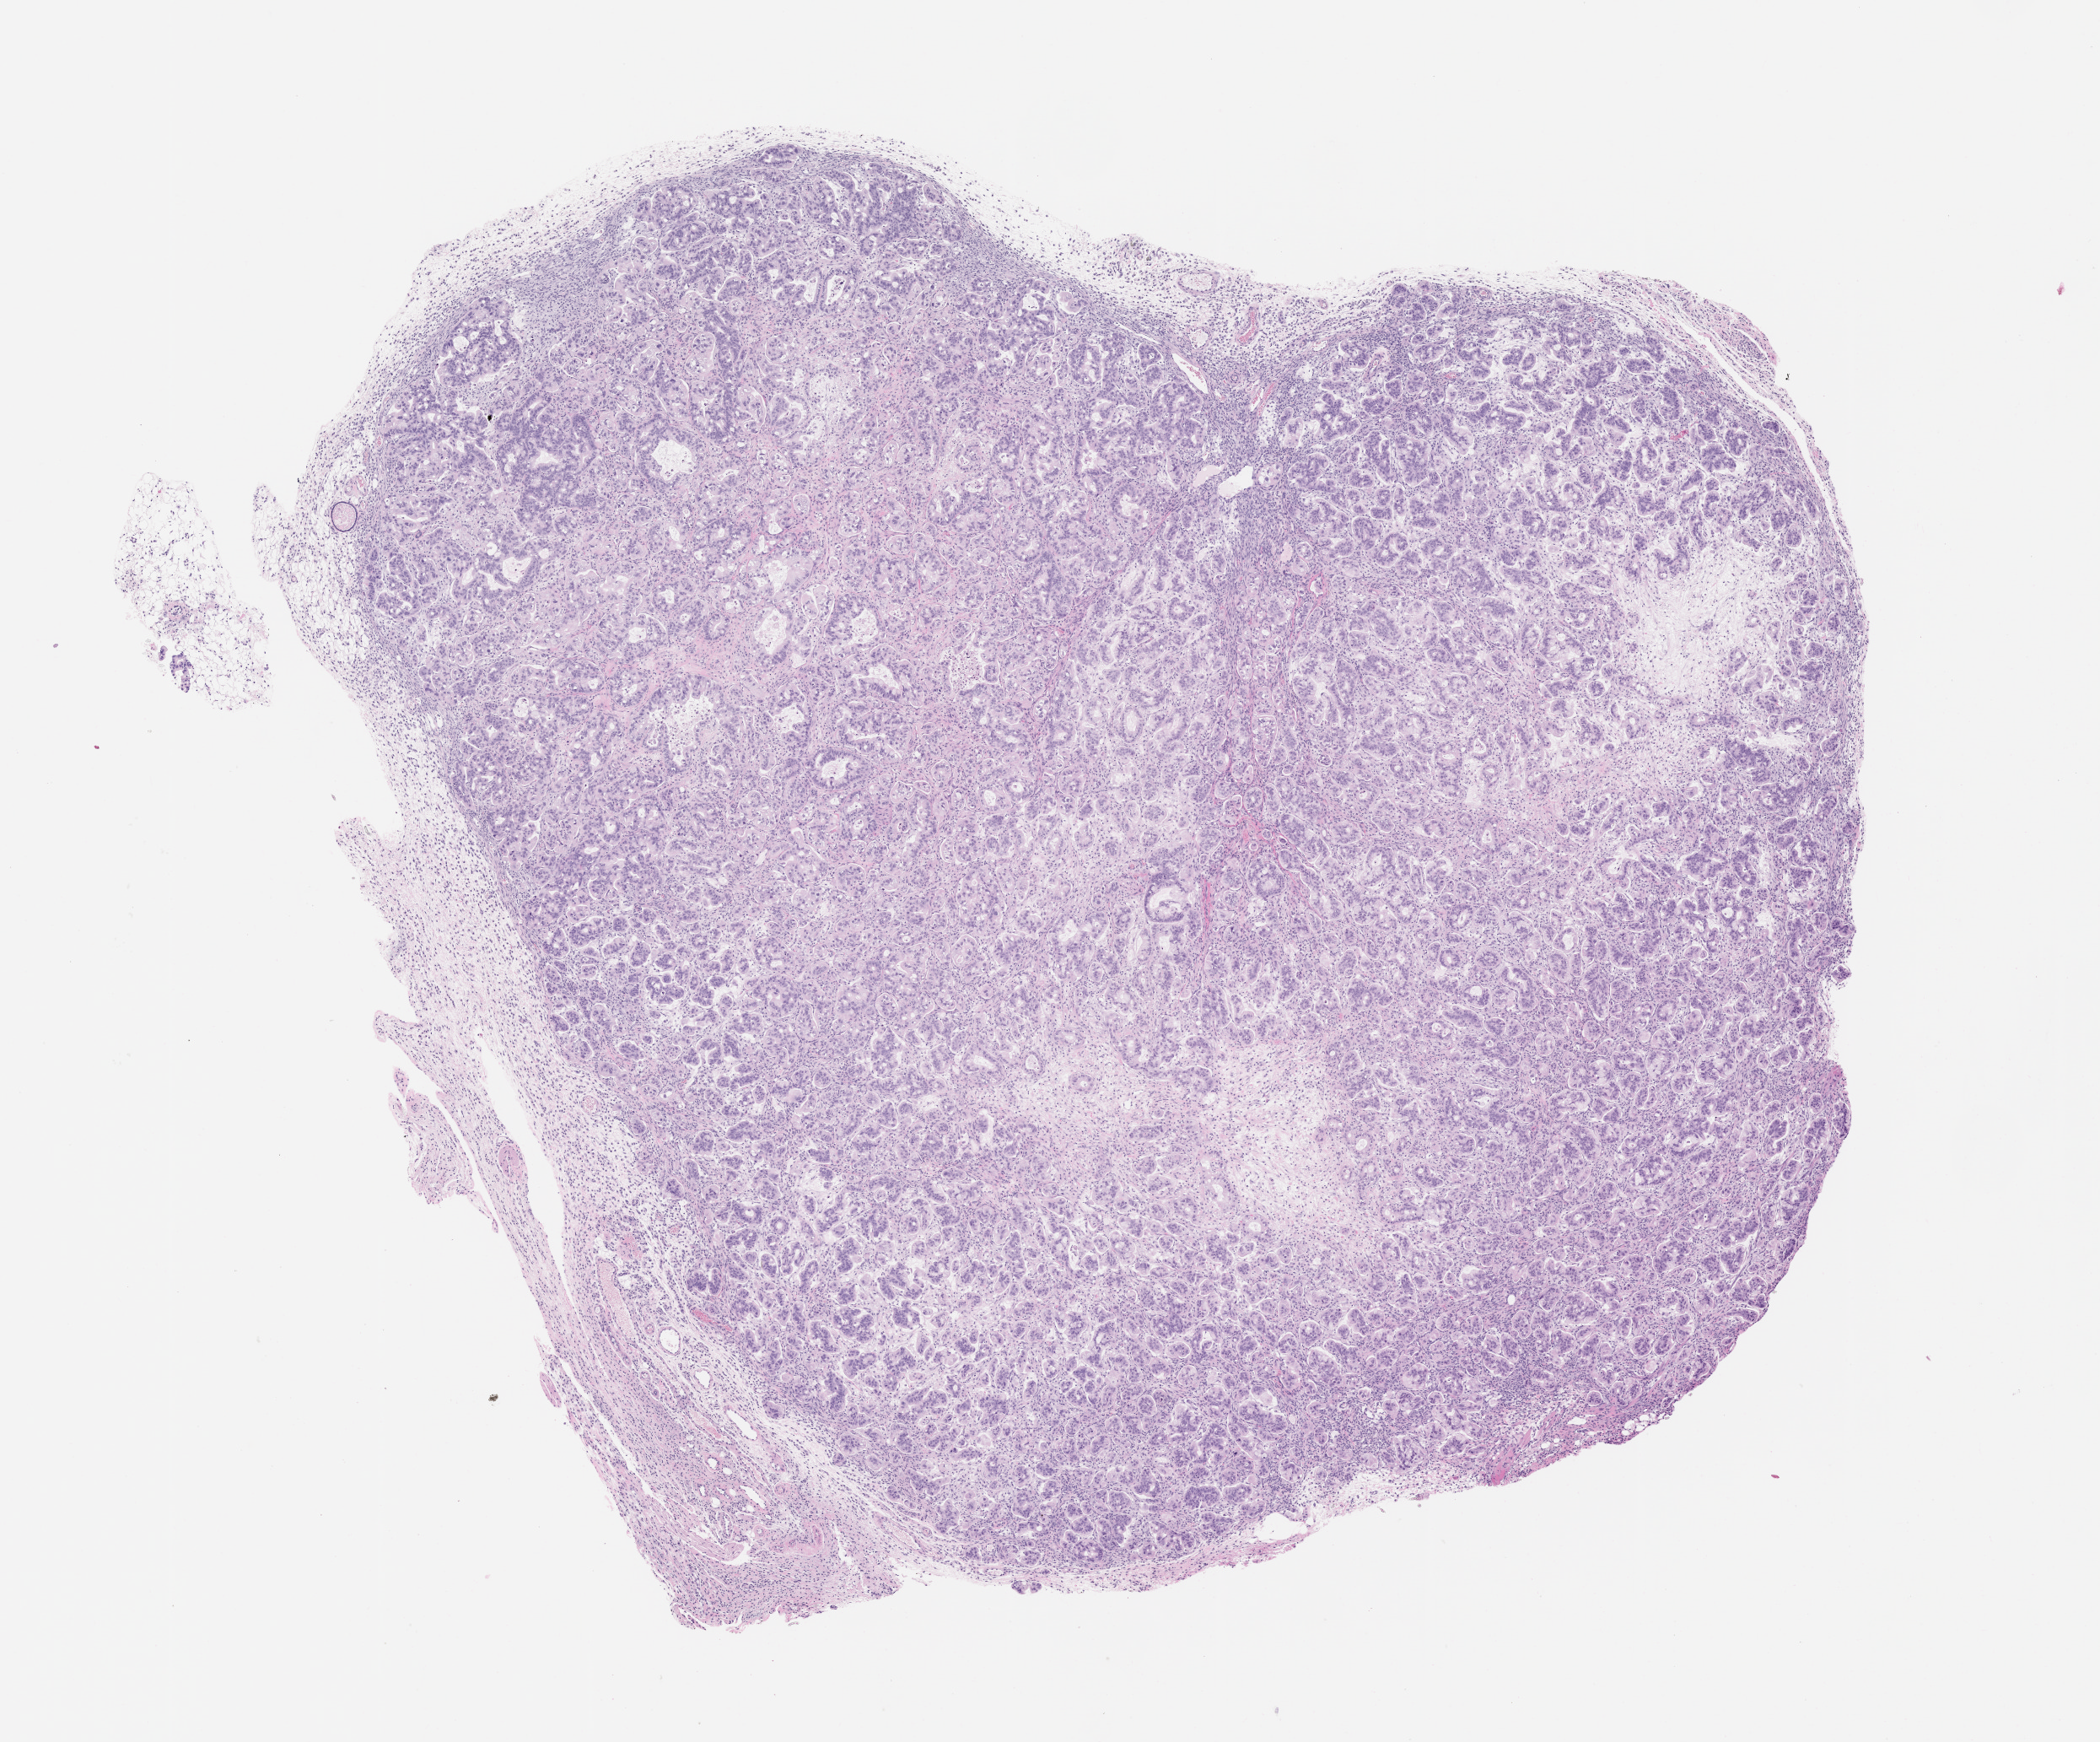
Whole-slide image, haematoxylin and eosin: patient-derived xenograft (human tumor grown in a mouse), passage 1 — low-resolution overview of the scanned area, about 10.0 x 8.3 mm. Formalin-fixed paraffin-embedded section. Originating tumor site category: pancreas.
Originating patient diagnosis: Pancreatic Adenocarcinoma.